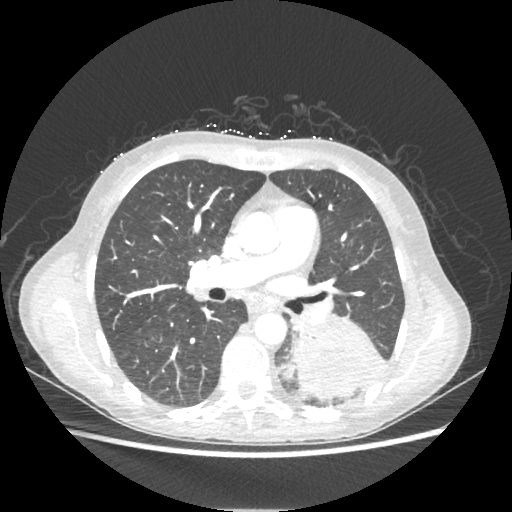
Chest CT, one axial slice; slice 122 of 221 in the series (ordered by position); reconstruction kernel STANDARD; lung window (W 1500 / L -600 HU); 512 × 512 image matrix, field of view 360 × 360 mm. Female patient, age 53 years. Case-level facts recorded for this patient, not image findings: clinical TNM (as recorded): T3 N0 M0.
Outlined on this slice (bounding box drawn by a radiologist):
- lung tumour (recorded histology: adenocarcinoma): bounding box <287,308,387,400> (left, top, right, bottom; pixels)